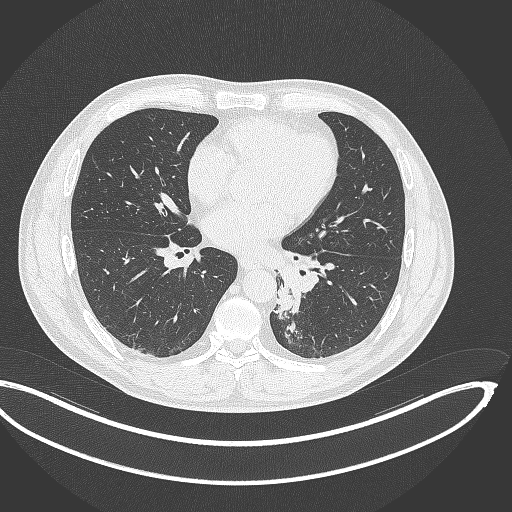
Chest CT, one axial slice; slice 159 of 362 in the series (ordered by position); reconstruction kernel B70f; 120 kVp; lung window (W 1500 / L -600 HU); 1 mm slice thickness; 512 × 512 image matrix. Patient: male, 50 years. From the clinical record (not read from this slice): clinical TNM (as recorded): T2a N3 M0.
Outlined on this slice (bounding box drawn by a radiologist):
- lung tumour (recorded histology: squamous cell carcinoma): box from (x=270, y=279) to (x=296, y=315) px